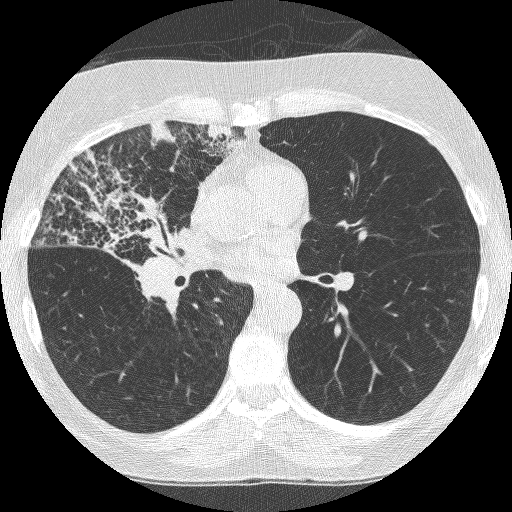
Low-dose screening chest CT, axial slice; third screening round (two years after baseline); lung window (W 1500 / L -600 HU); lung (sharp) reconstruction kernel (BONE); slice 138 of 253 in the series; 512 × 512 image matrix. Female, age 64 years at enrolment. Former smoker at enrolment.
Expert-annotated lung lesion, bounding box <60,169,200,312> (left, top, right, bottom; pixels). Screening reader's record for this exam (one nodule recorded; not confirmed to be the boxed lesion): non-calcified nodule or mass ≥4 mm, right upper lobe, 49 × 43 mm, spiculated (stellate) margins, soft tissue attenuation, pre-existing on the prior screen: yes; interval growth: yes. Official screen result: positive, other. Later outcome: lung cancer diagnosed 7 days after this screen — adenocarcinoma, NOS, right upper lobe, right middle lobe, right hilum, stage IV (AJCC 6th edition), 85 mm at pathology.